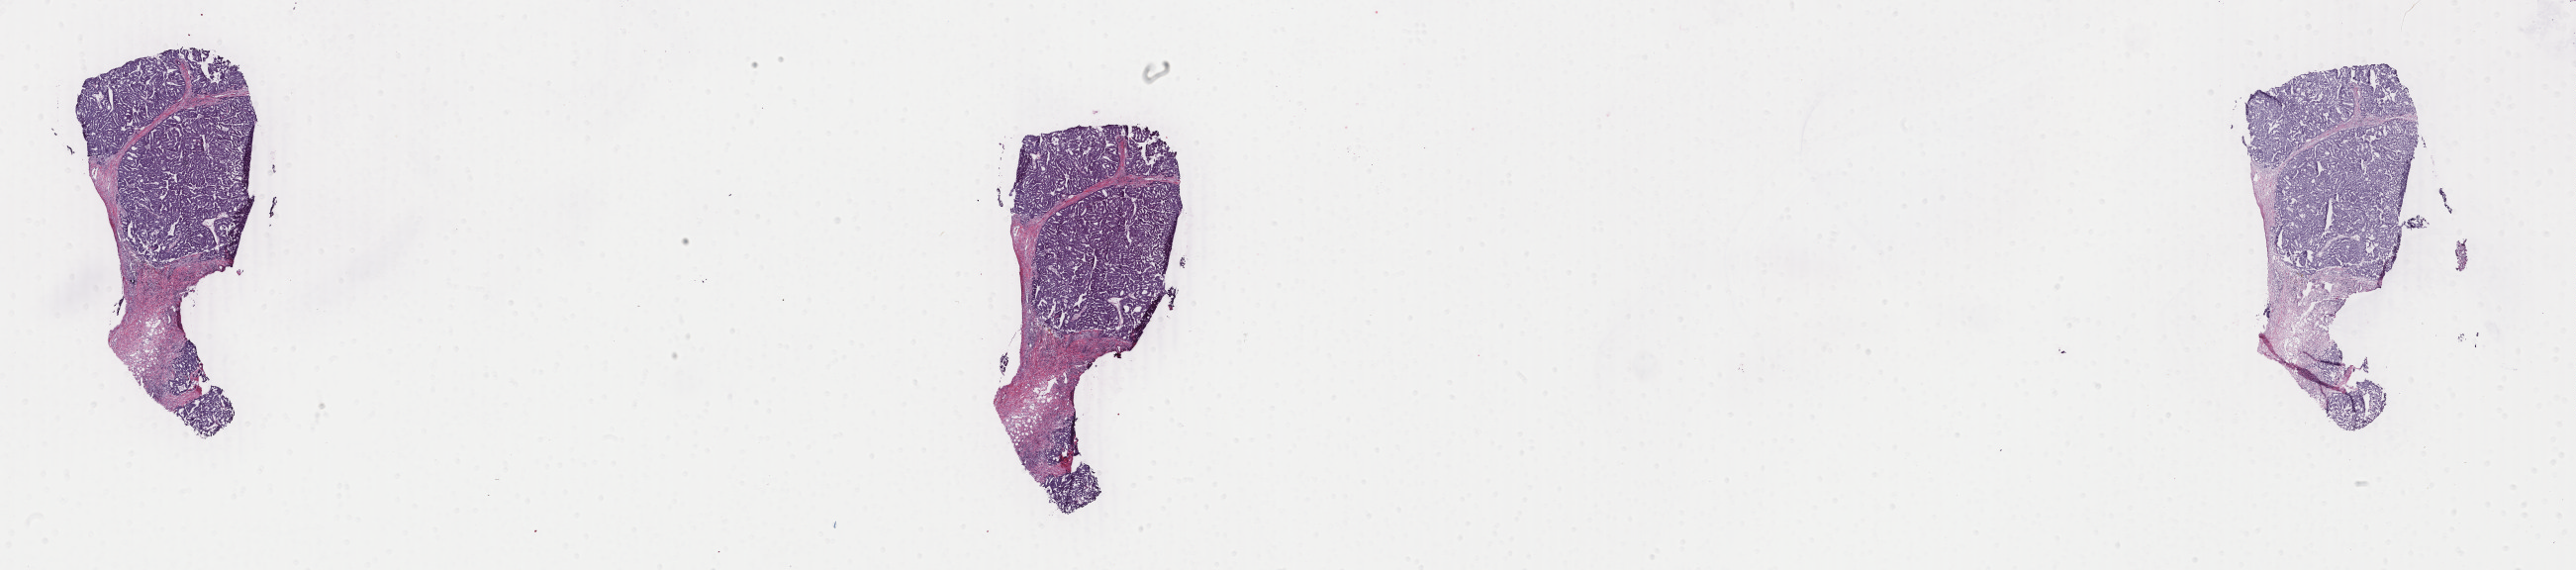
Whole-slide histology image, H&E — a low-resolution overview of the entire scanned area, about 41.4 x 9.2 mm; frozen section from the bottom of the tissue portion; sample: primary tumour, breast. Patient sex: female. Slide review estimates, as recorded: tumour cells 85%, tumour nuclei 85%, normal cells 0%, stromal cells 15%, necrosis 0%. Infiltration values recorded for this section: lymphocyte infiltration 1%, monocyte infiltration 0%, neutrophil infiltration 0%.
Diagnosis: Intraductal papillary adenocarcinoma with invasion.